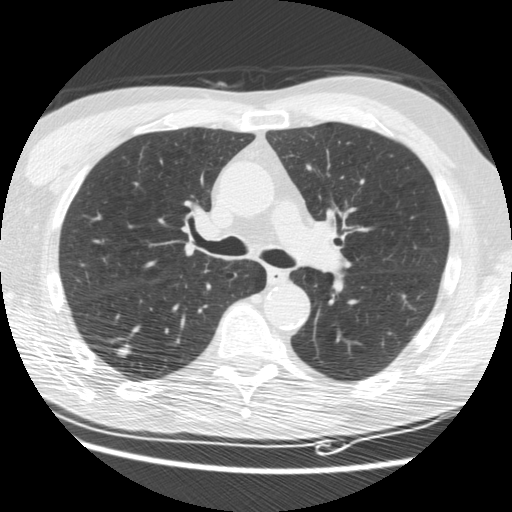
Low-dose screening chest CT, axial slice, third screening round (two years after baseline), lung window (W 1500 / L -600 HU), 120 kVp, 512 × 512 image matrix. Male, age 62 years at enrolment. Current smoker at enrolment.
Lesion marked by an expert reader, bounding box <98,332,144,373> (left, top, right, bottom; pixels). The screening reader recorded 3 non-calcified nodules or masses ≥4 mm on this exam; which of them this box marks is not recorded. Official screen result: positive, other. Participant outcome: lung cancer diagnosed 33 days after this screen — adenocarcinoma, NOS, right lower lobe, moderately differentiated (G2), stage IIIB (AJCC 6th edition), 15 mm at pathology.